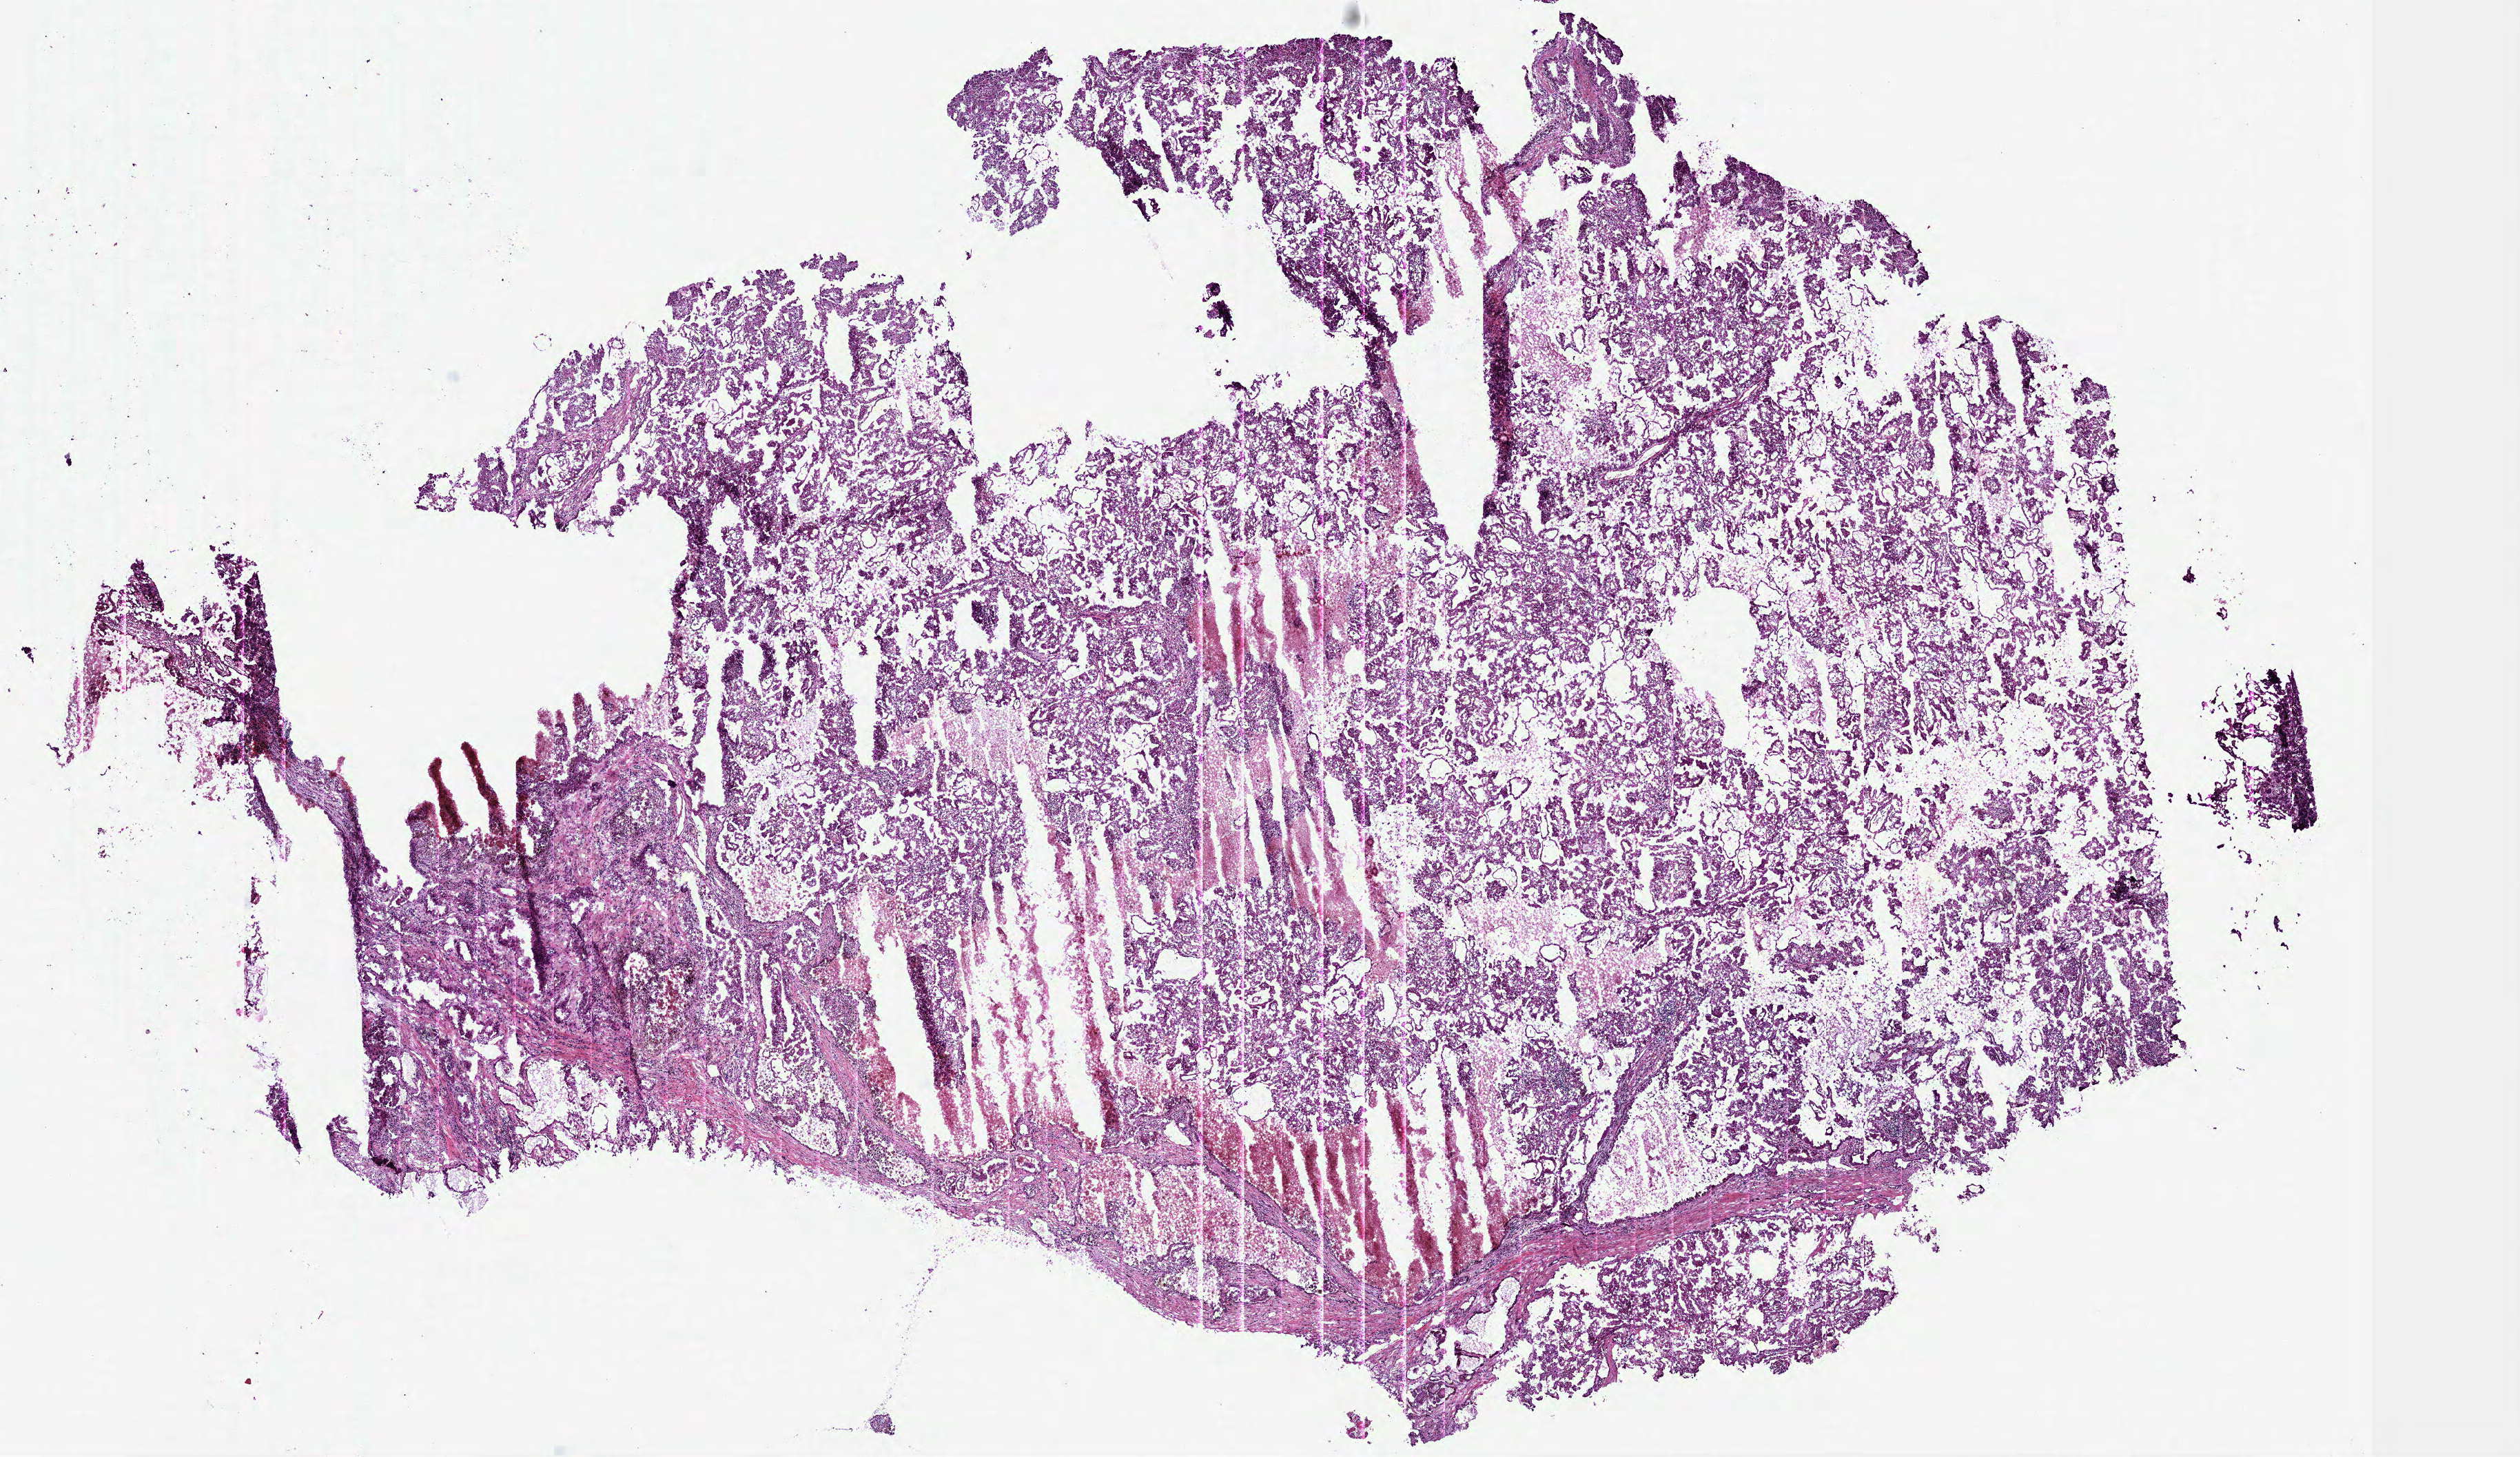
Whole-slide histology image, H&E, low-resolution overview of the scanned area, about 14.7 x 8.5 mm (acquisition: 40x scan); frozen section from the bottom of the tissue portion; kidney, primary tumour sample. Patient: male, age at initial diagnosis 79 years. Composition of this section per pathologist review: tumour cells 82%, tumour nuclei 75%, normal cells 0%, stromal cells 10%, necrosis 18%.
AJCC pathologic stage: III. Diagnosis: Papillary adenocarcinoma, NOS.